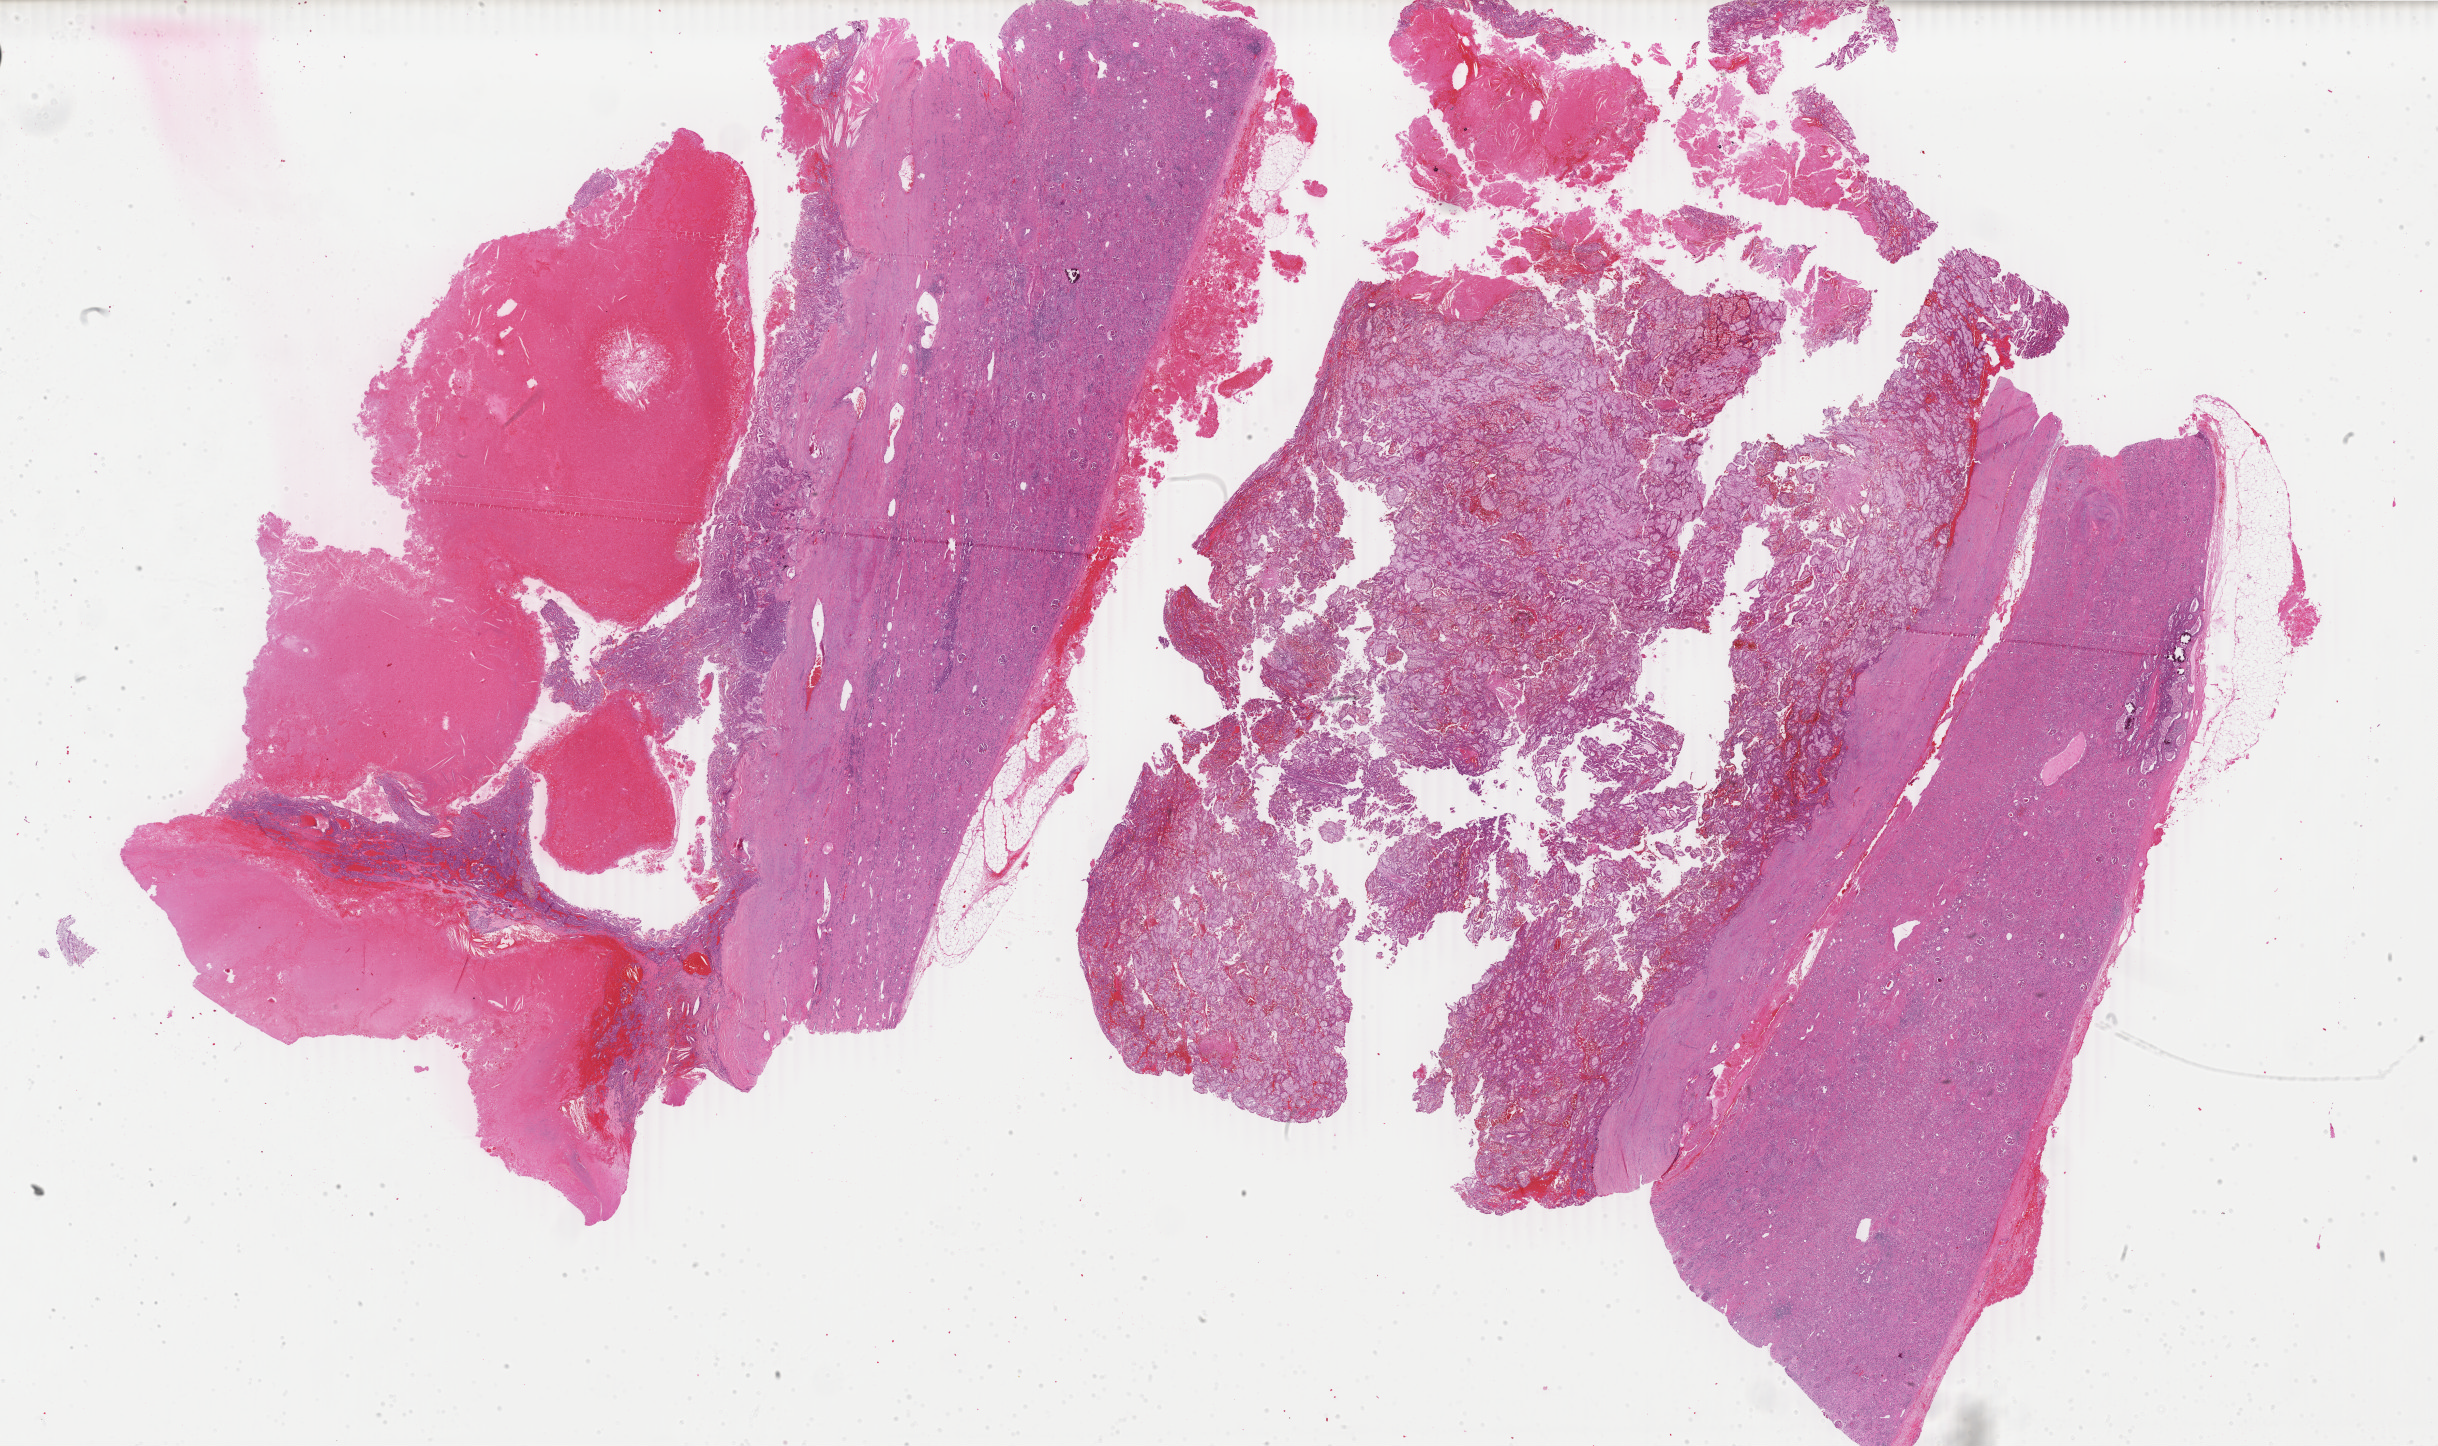
Digitized H&E tissue section (whole slide) — a low-resolution overview of the entire scanned area, about 38.8 x 23.0 mm (slide scanned at 40x). Formalin-fixed paraffin-embedded (FFPE) diagnostic section. Primary tumour sample from the kidney. Patient: male, age at initial diagnosis 53 years.
- pathologic diagnosis: Papillary adenocarcinoma, NOS
- AJCC pathologic stage: II